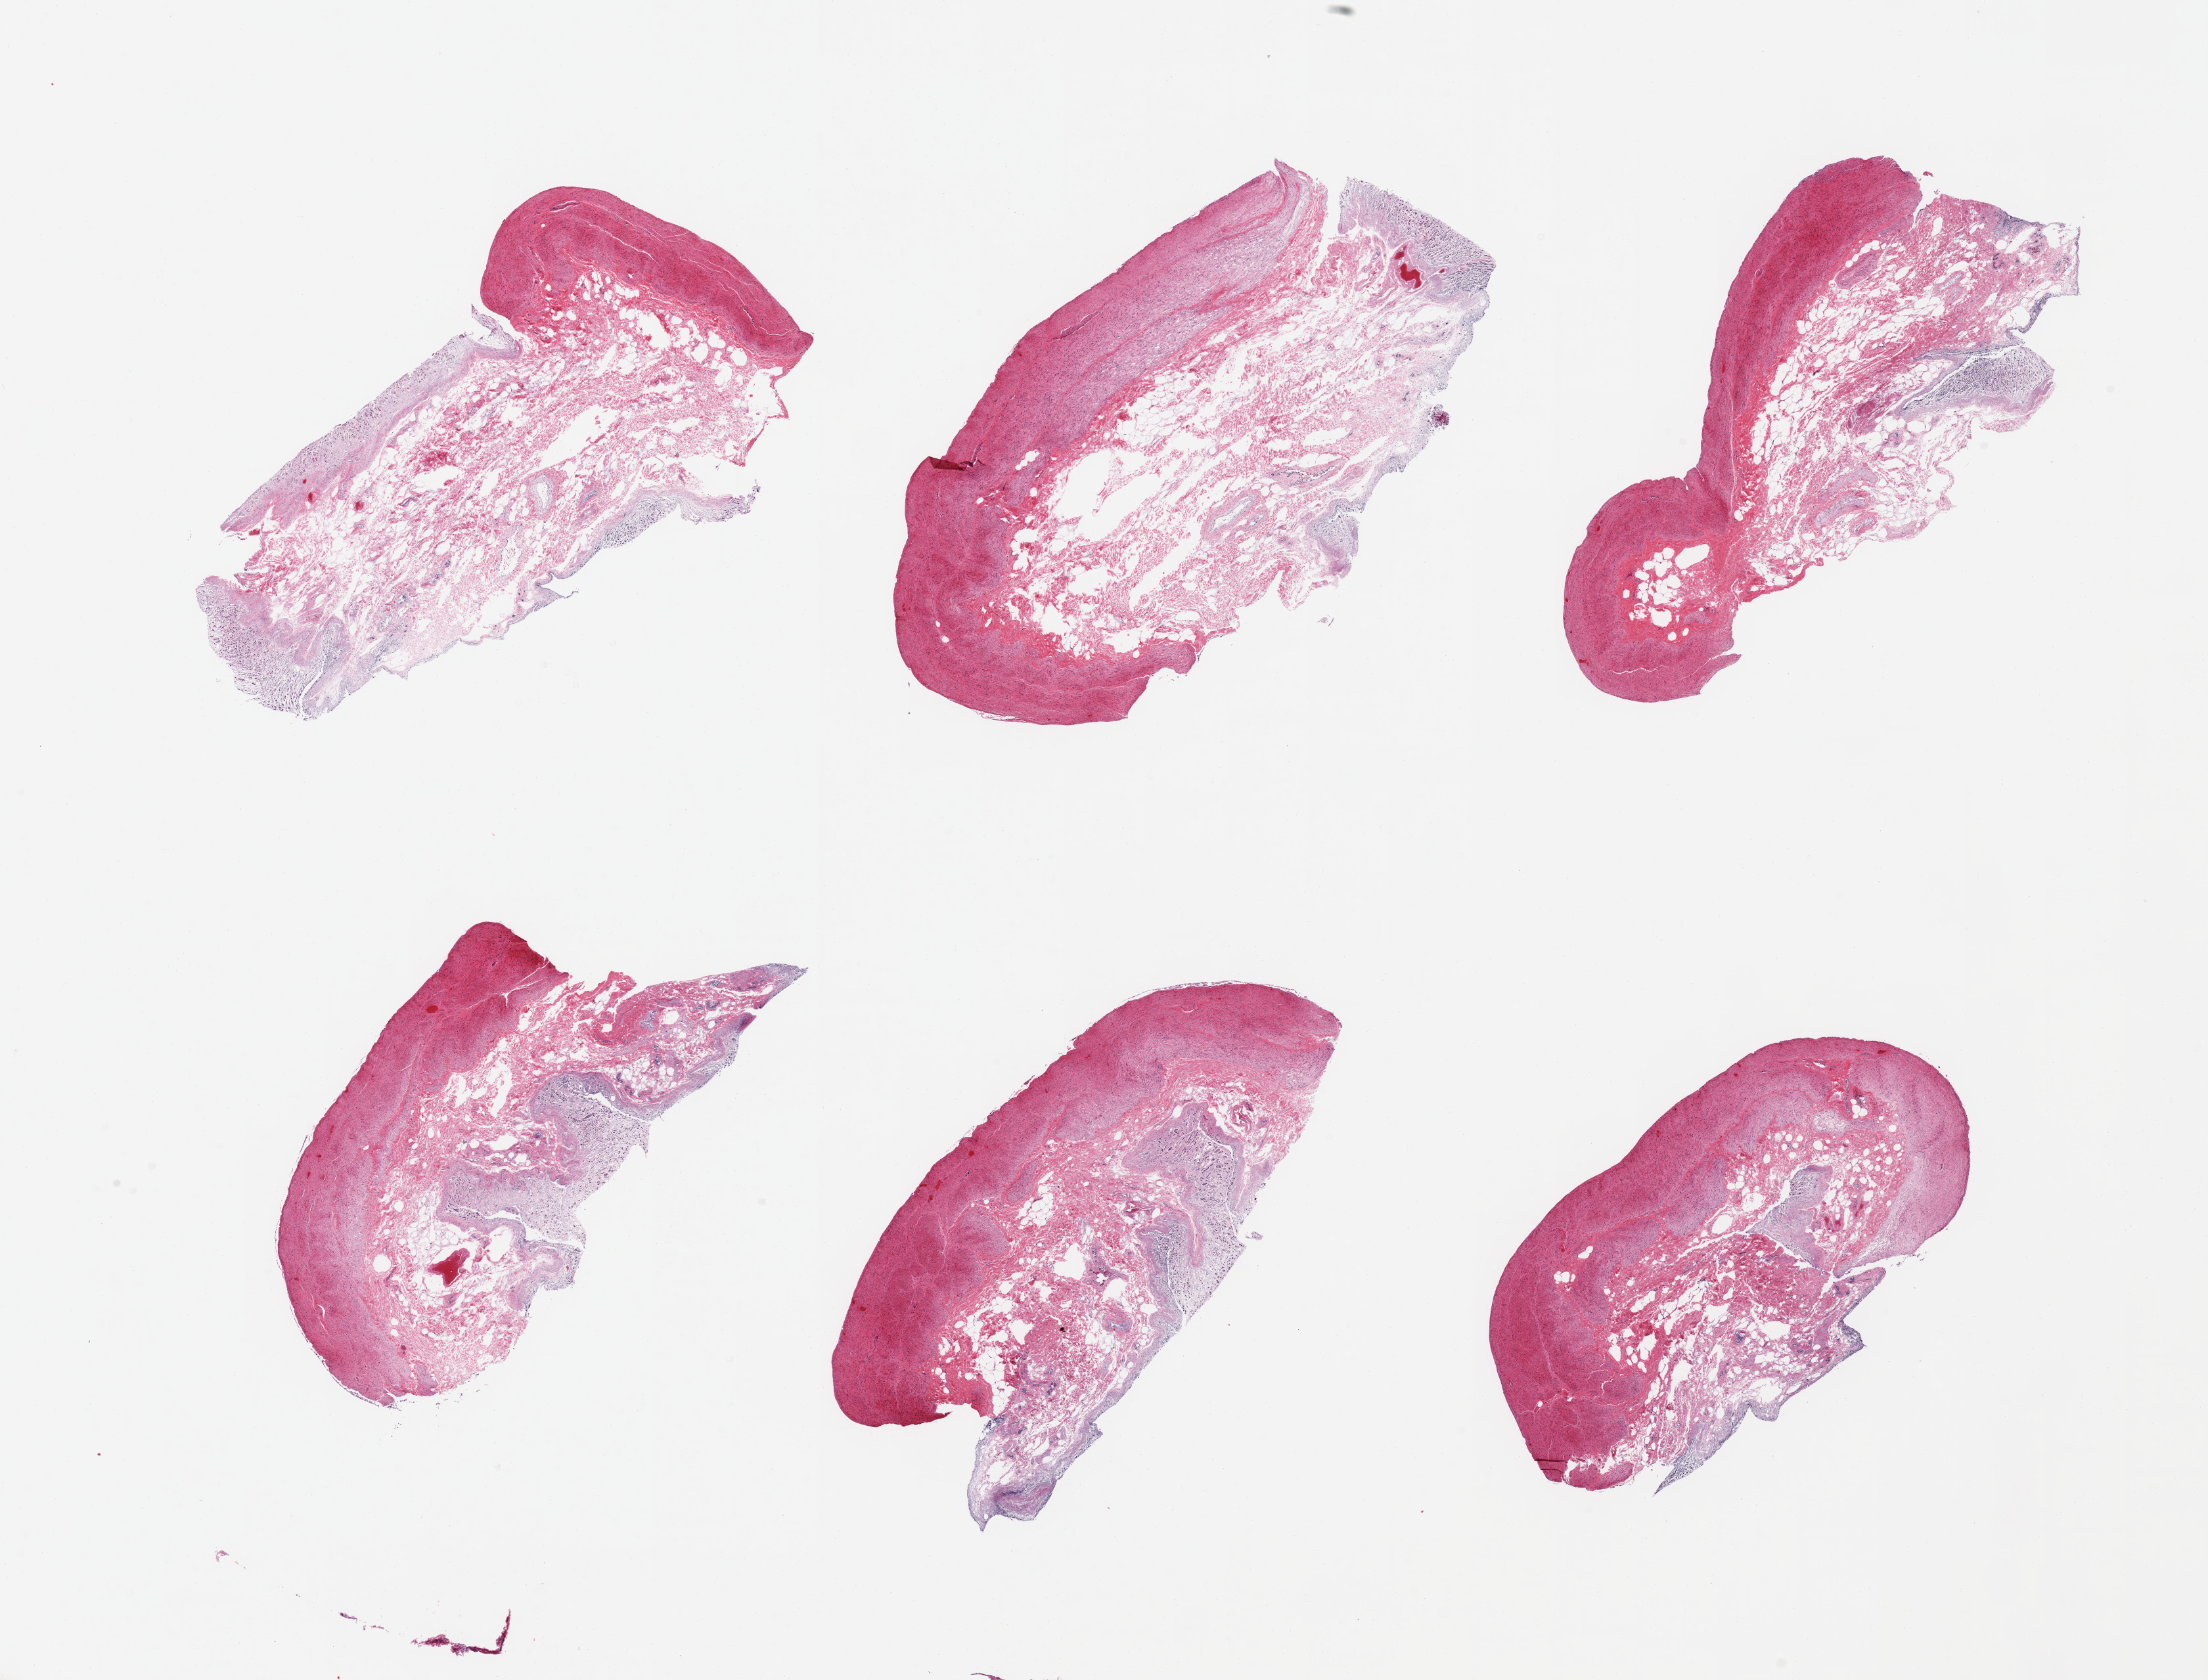
Digitized hematoxylin and eosin (H&E)-stained section — shown as a low-resolution overview of the whole scanned area (about 26.6 x 20.2 mm, from a 20x scan). PAXgene-fixed paraffin-embedded (PFPE) section. Target tissue: stomach. Tissue donor sample.
Reviewer comment on this tissue sample: 6 pieces, target mucosa up to ~0.5mm advanced autolysis.